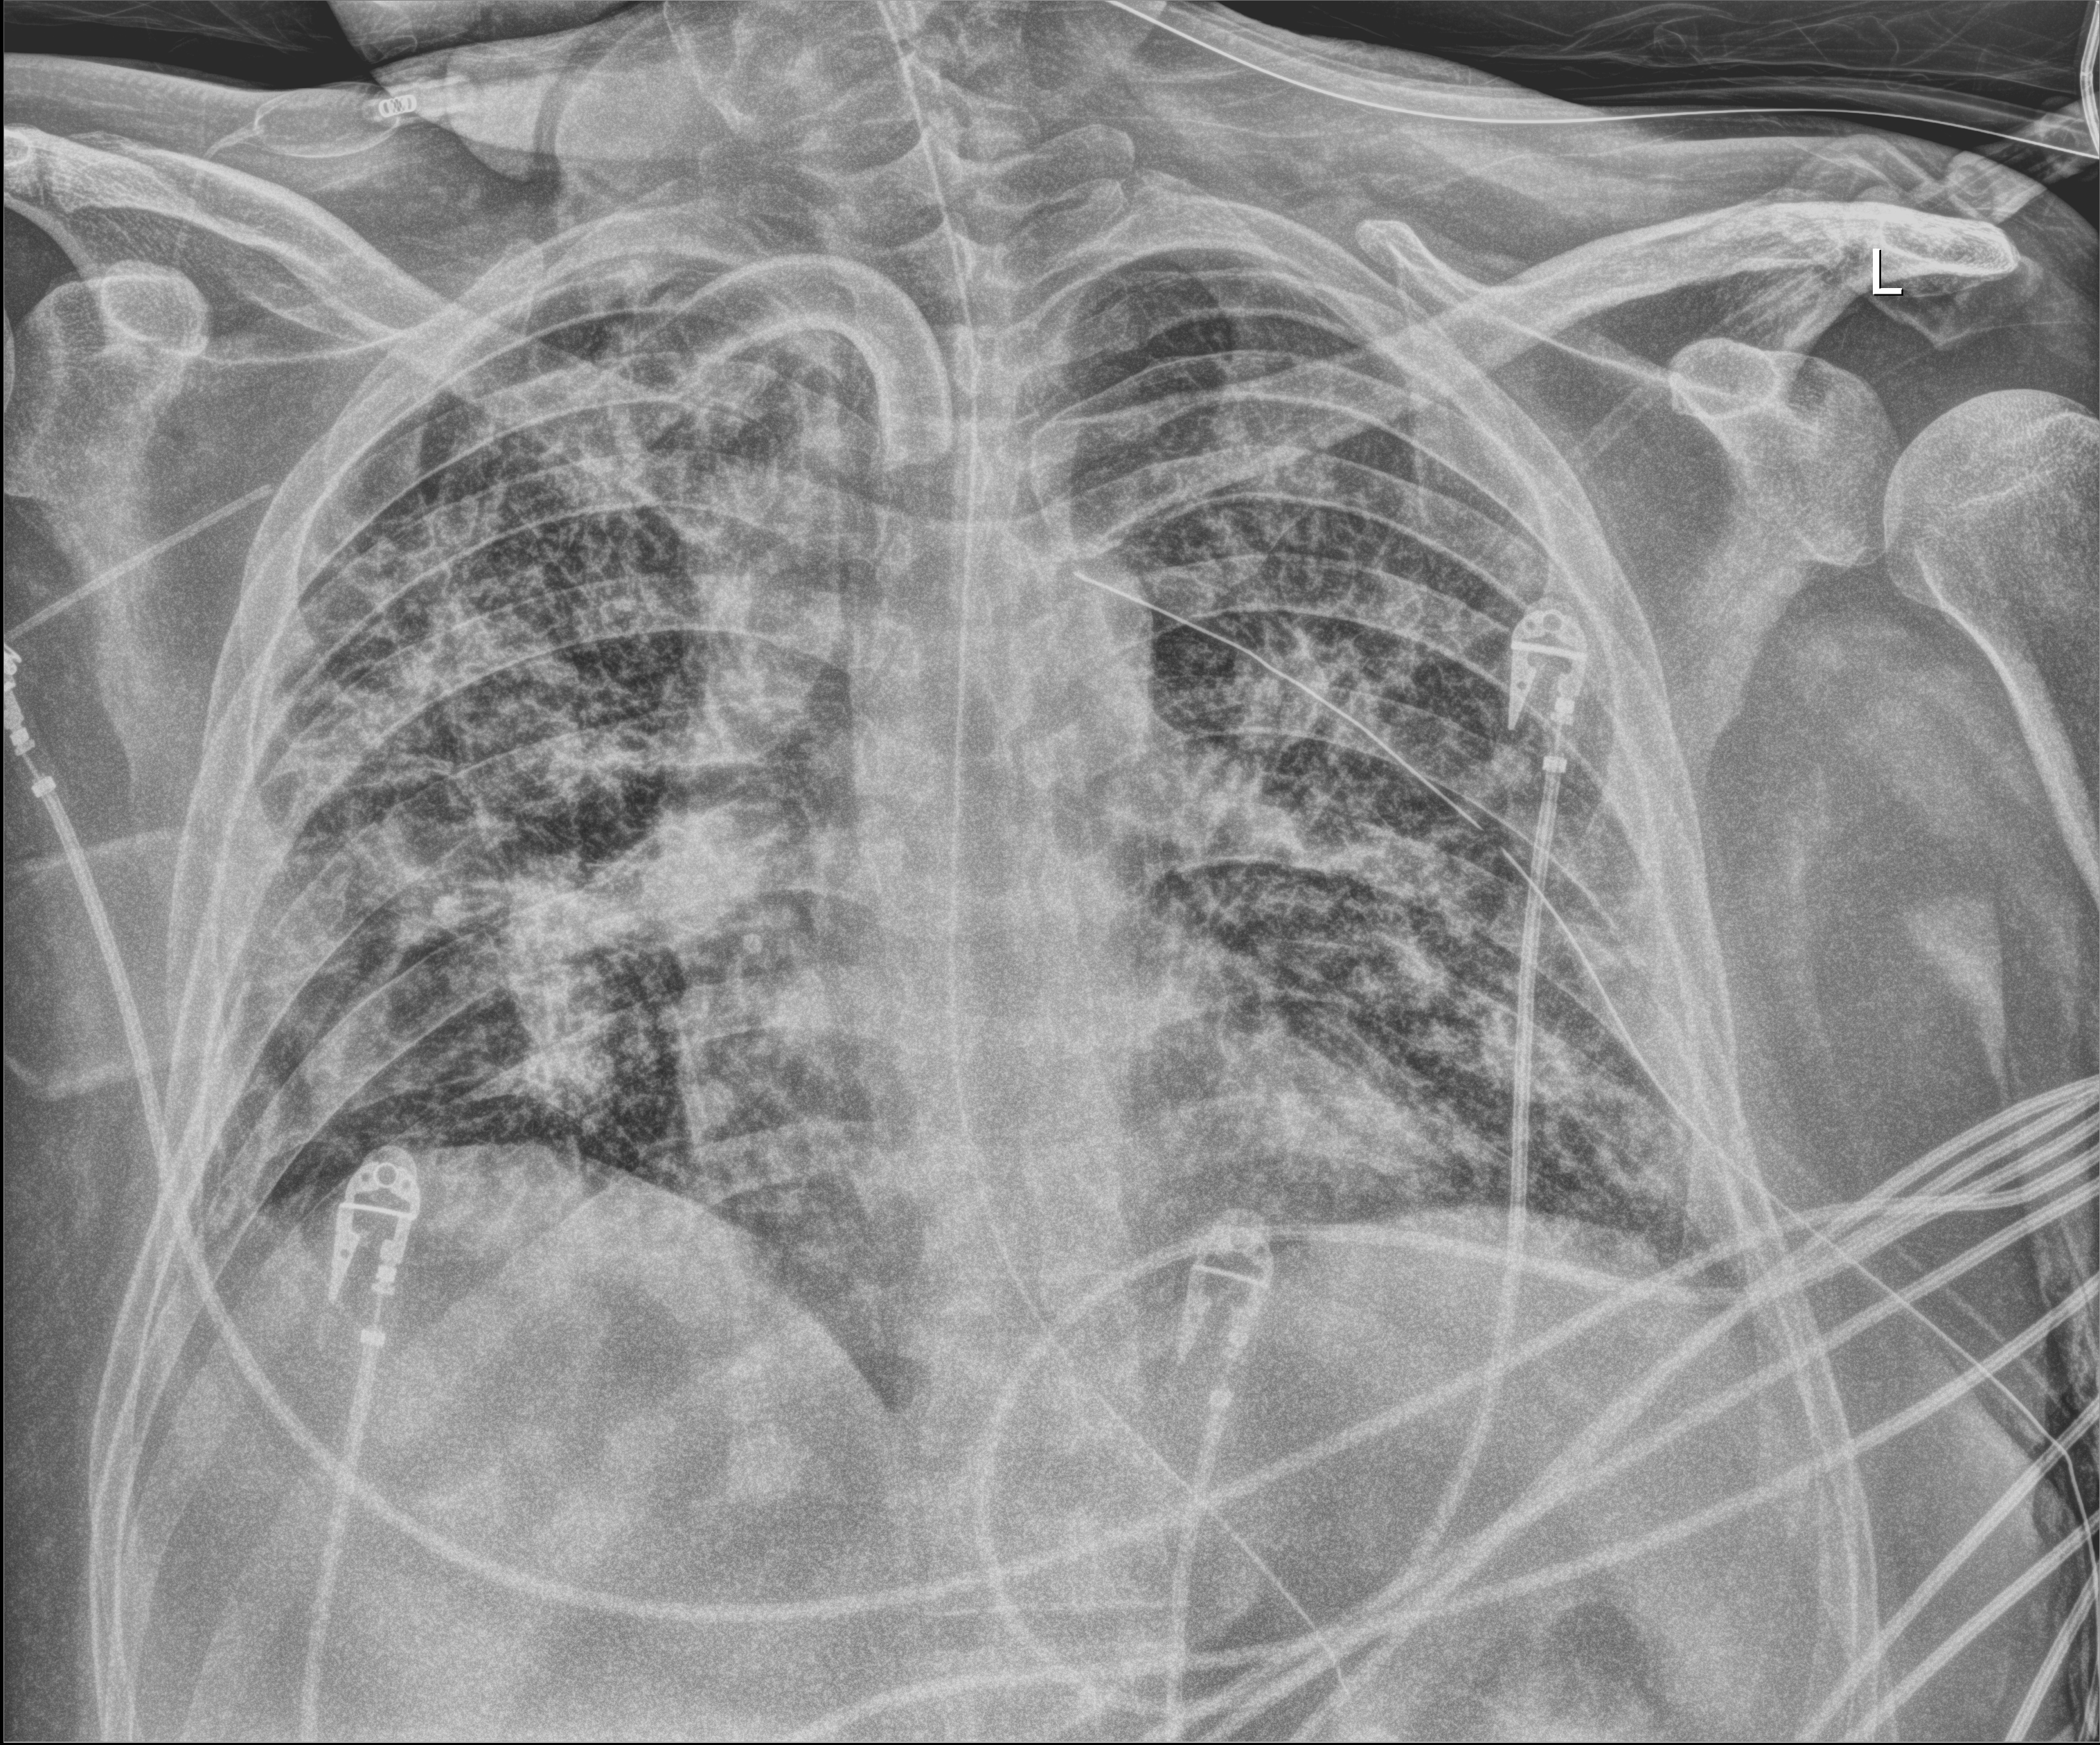
Chest X-ray (portable), anteroposterior (AP) projection. Male patient hospitalised with COVID-19, age 18–59 years.
Hospital-stay facts (about this admission, not read from this image; timing relative to this image not recorded):
- diabetes (admission record): yes
- length of hospital stay: 63 days